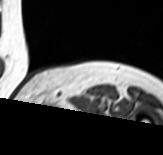
MRI of an extremity soft-tissue mass, one axial slice; MR volume resampled by the dataset authors to the PET/CT grid (not the native acquisition matrix); 3.27 mm slice thickness; 163 × 155 image matrix, field of view 159 × 151 mm. Female patient. From the clinical record (not read from this slice): histological type: pleomorphic leiomyosarcoma; grade: high; site of the primary tumour: left thigh.
Outlined on this slice (expert contour drawn on MRI and transferred to this co-registered scan by the dataset authors):
- gross tumour volume including surrounding oedema: bounding box (x1, y1, x2, y2) in pixels: (42, 104, 63, 121)